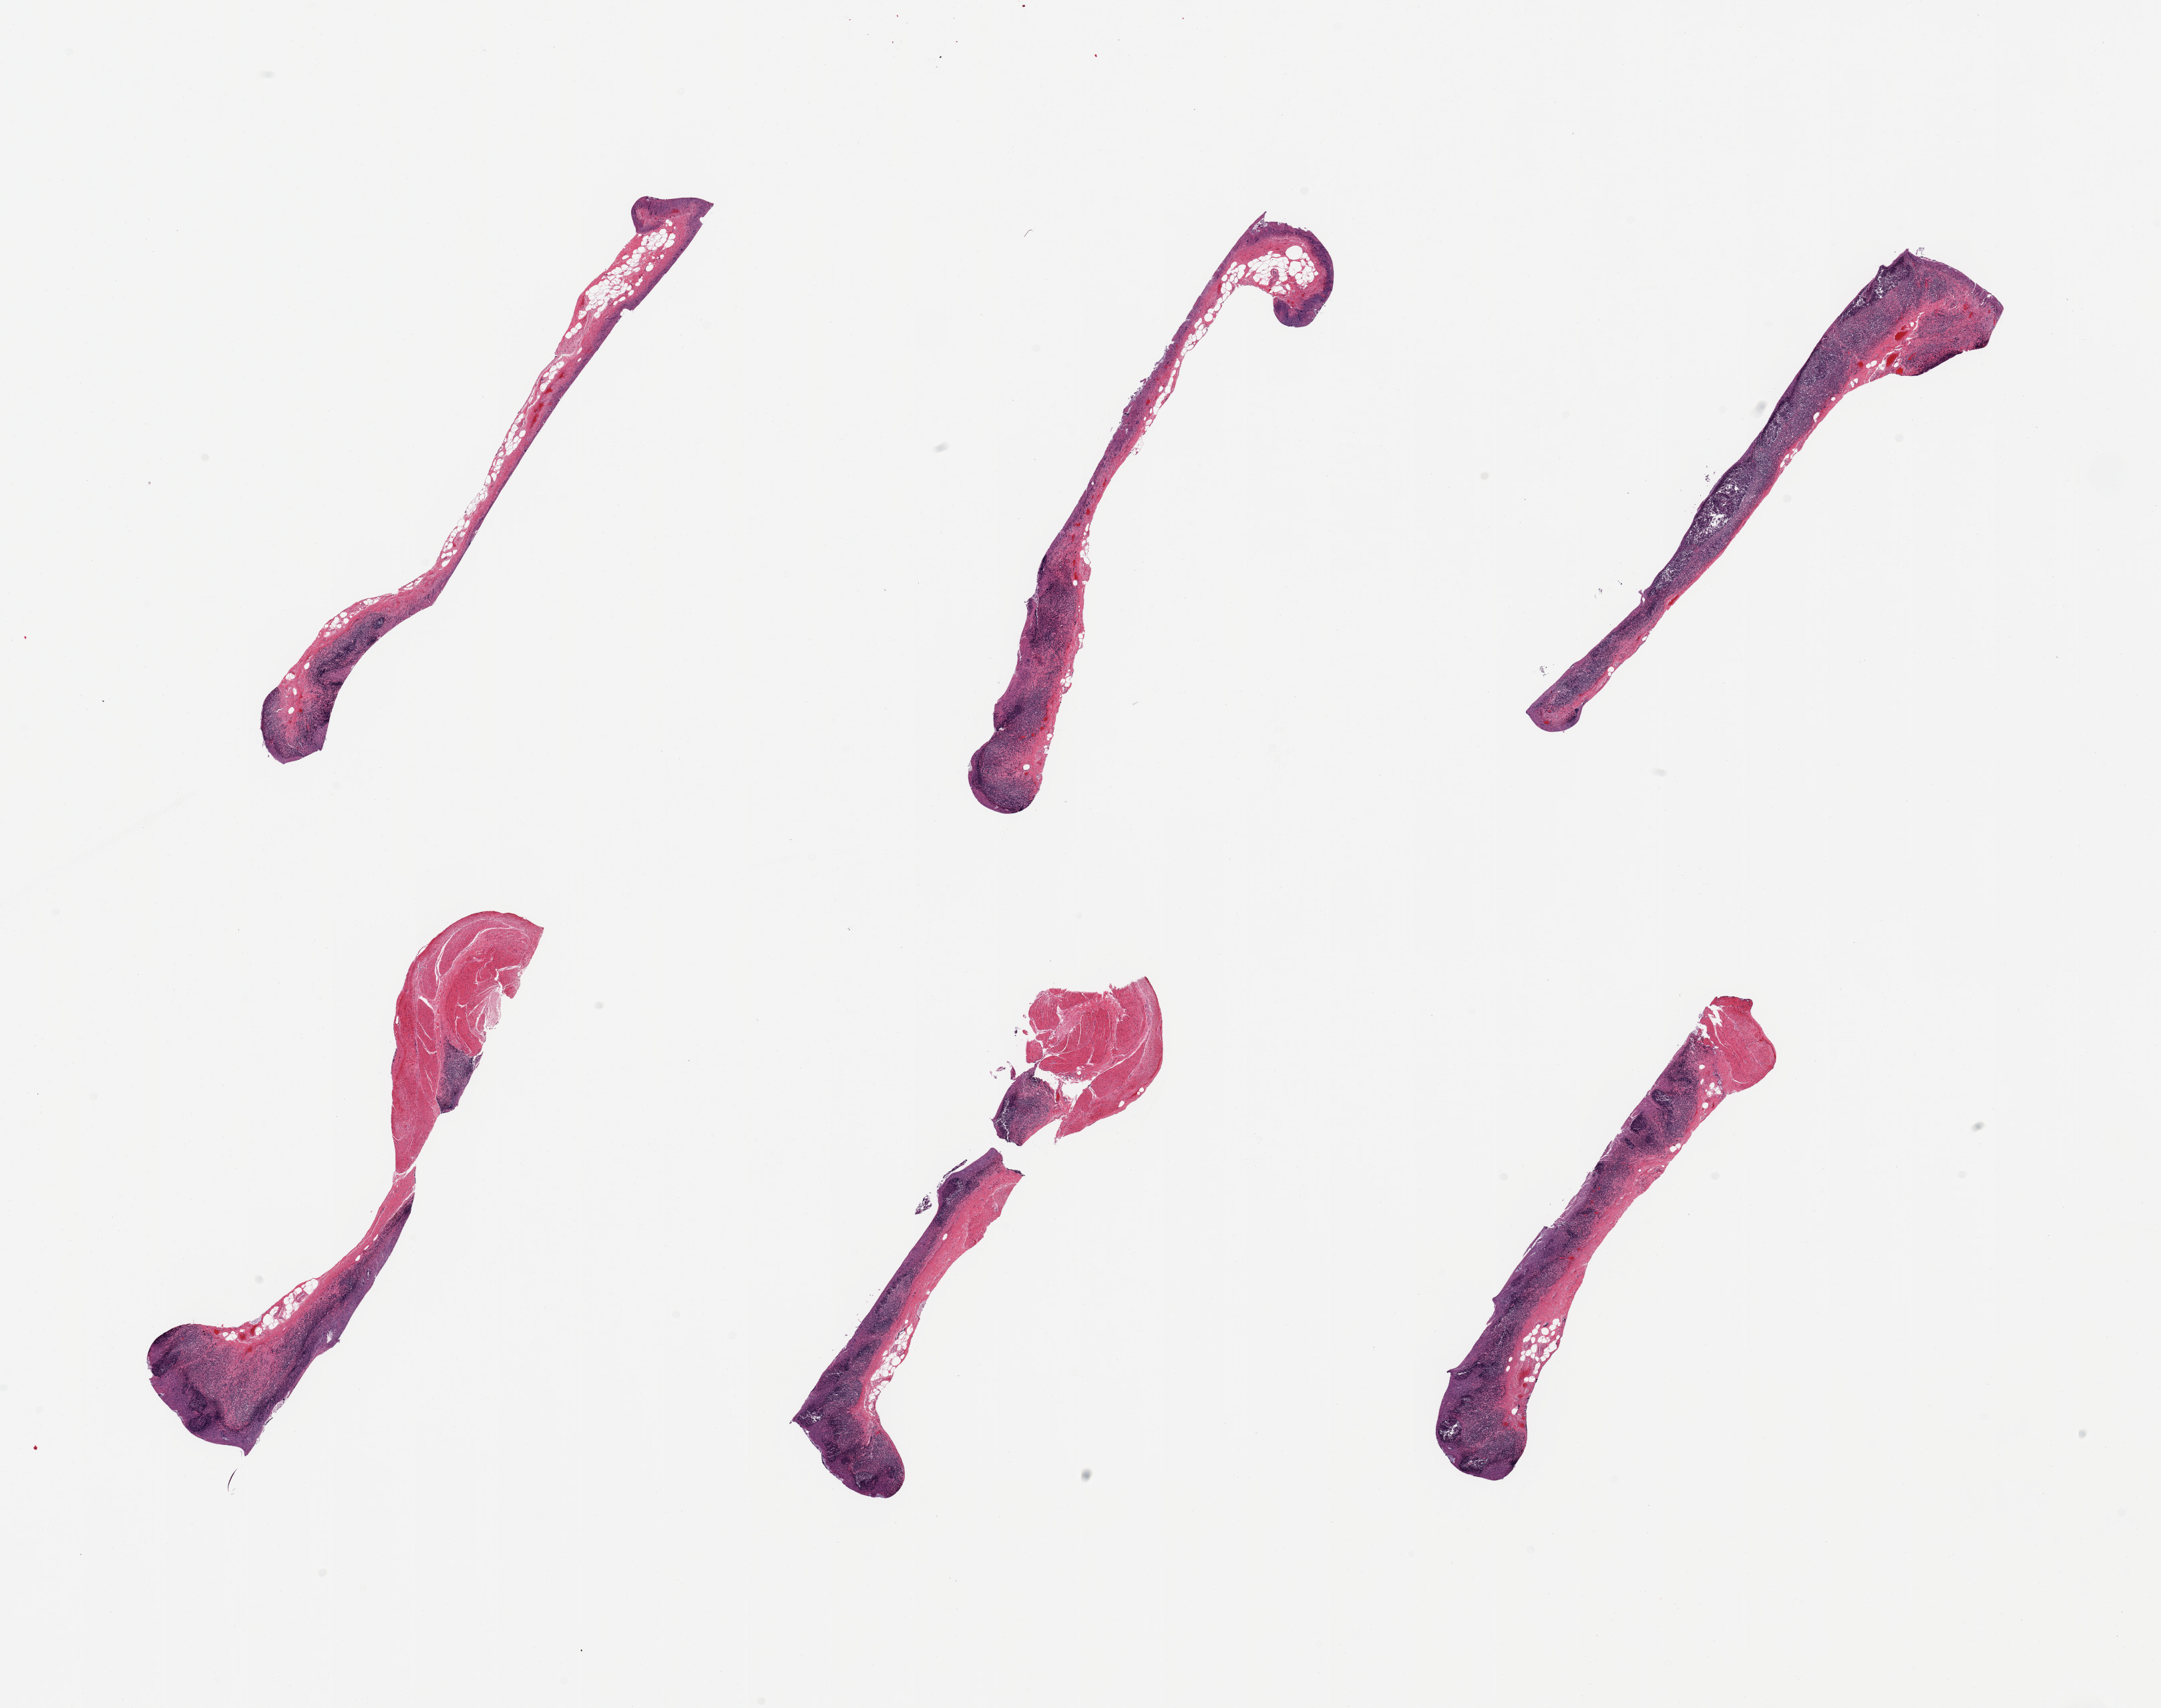
Whole-slide image, hematoxylin and eosin (H&E) stain — shown as a low-resolution overview of the whole scanned area (about 25.6 x 20.2 mm); PAXgene-fixed, paraffin-embedded tissue; target tissue: ileum; donor tissue sample. Male donor.
• pathologist's review note for this sample: 6 pieces; well dissected partly autolyzed, but abundant lymphoid tissue with small amount of muscularis propria